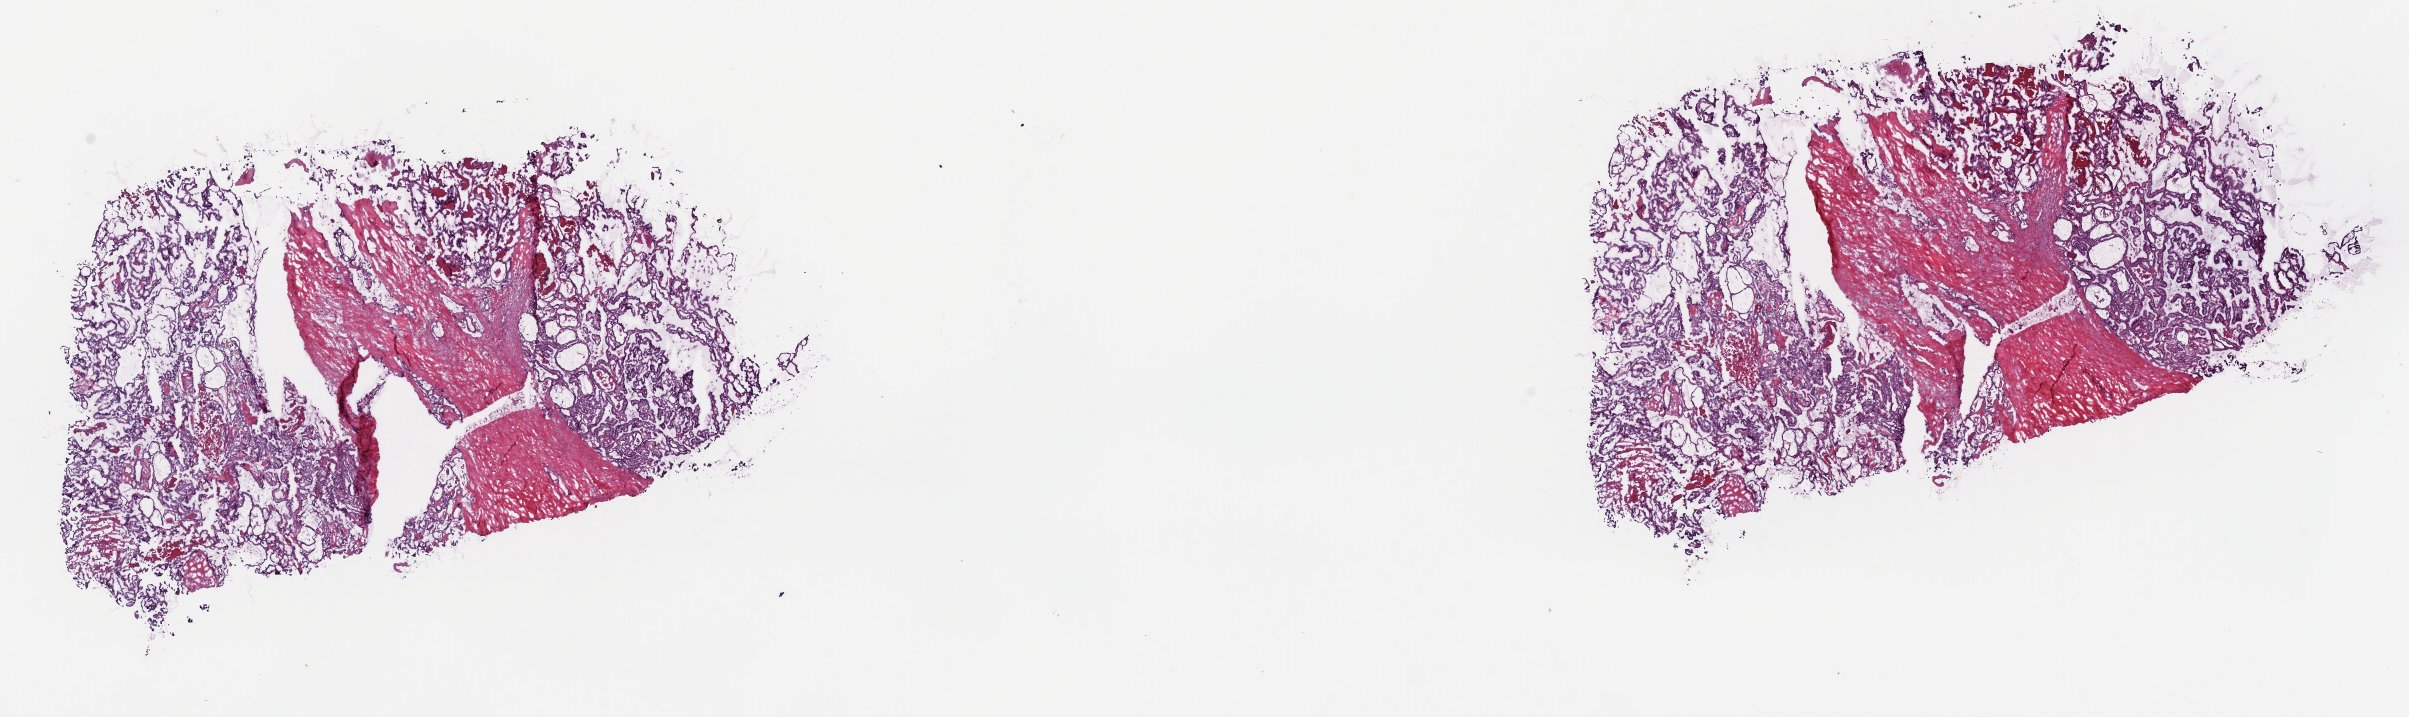
Digitized Hematoxylin and eosin (H&E) stained tissue section (whole slide) — low-resolution overview of the scanned area, about 19.0 x 5.7 mm; frozen section; sample: primary tumour, thyroid. Male patient; age at initial diagnosis 33 years. Slide review estimates, as recorded: tumour cells 75%, tumour nuclei 85%, normal cells 0%, stromal cells 25%, necrosis 0%. Inflammatory infiltration, as recorded: lymphocyte infiltration 0%, monocyte infiltration 0%, neutrophil infiltration 0%.
AJCC pathologic stage: I. Lymph nodes positive (case pathology): 5 of 5 examined. Diagnosis: Papillary adenocarcinoma, NOS (thyroid gland). Laterality: left.